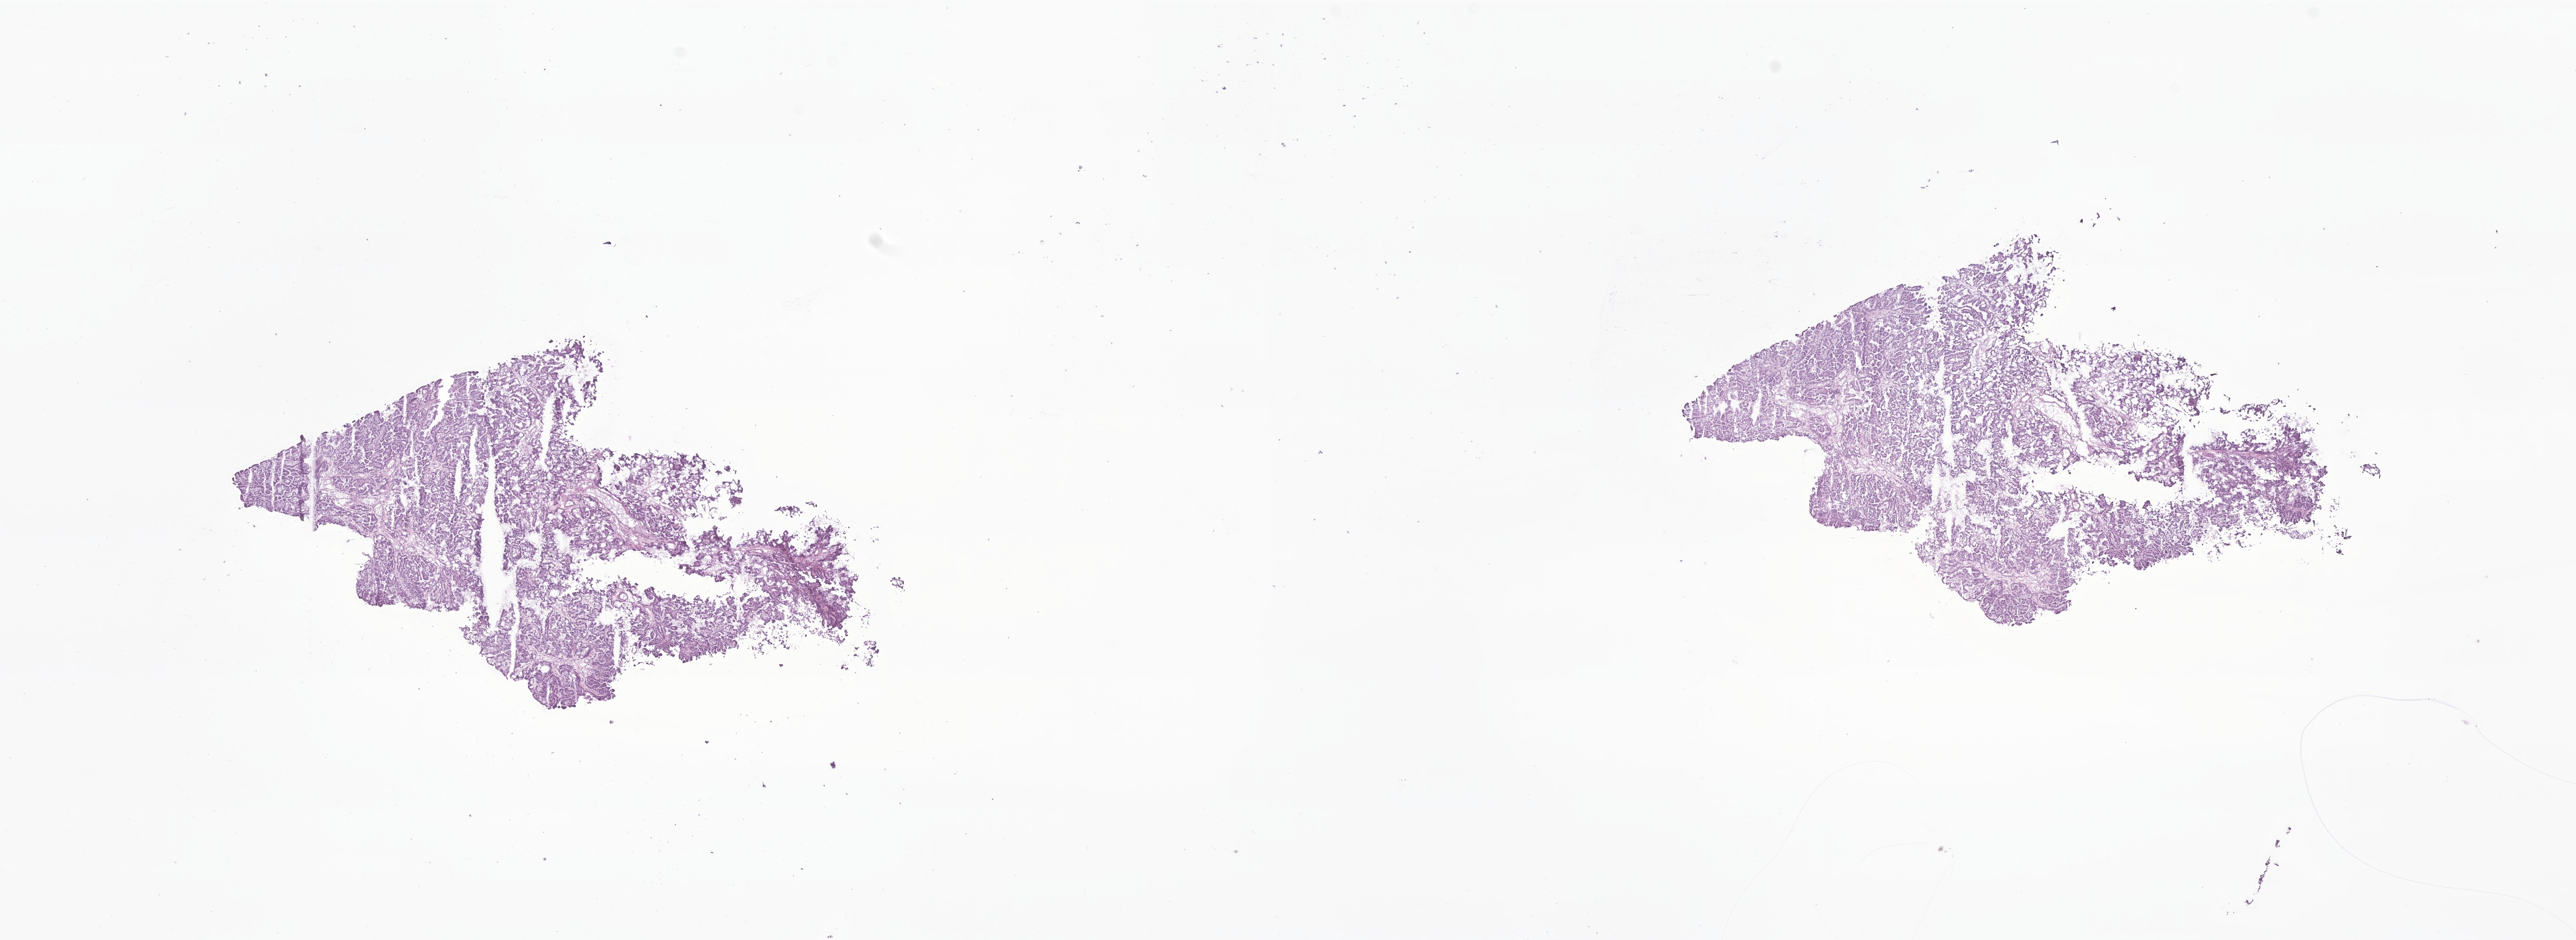
Whole-slide image, H&E stain of tumor tissue from the brain — whole scanned area (about 20.6 x 7.5 mm) shown as a low-resolution overview, frozen section. Patient: male, age 504 days (about 1.4 years).
Recorded diagnosis: Choroid plexus papilloma, NOS.